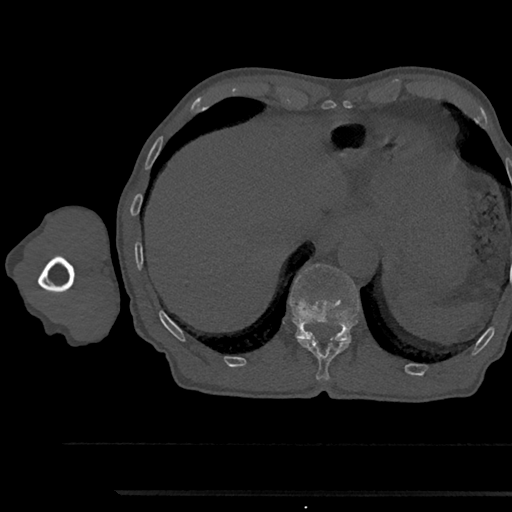
CT including the spine, one axial slice. Position 751 of 797 along the scan axis. Reconstruction kernel Br40s/3. 120 kVp. Bone window (W 1800 / L 400 HU). 0.5 mm slice thickness. 512 × 512 image matrix, field of view 367 × 367 mm. Male patient, age 79 years. Case-level facts recorded for this patient, not image findings: primary cancer: prostate.
Structures marked on this image (semi-automatic segmentation, software-assisted and operator-edited):
- T11 vertebra: bounding box <299,339,349,380> (left, top, right, bottom; pixels)
- T12 vertebra: <289,264,360,342>